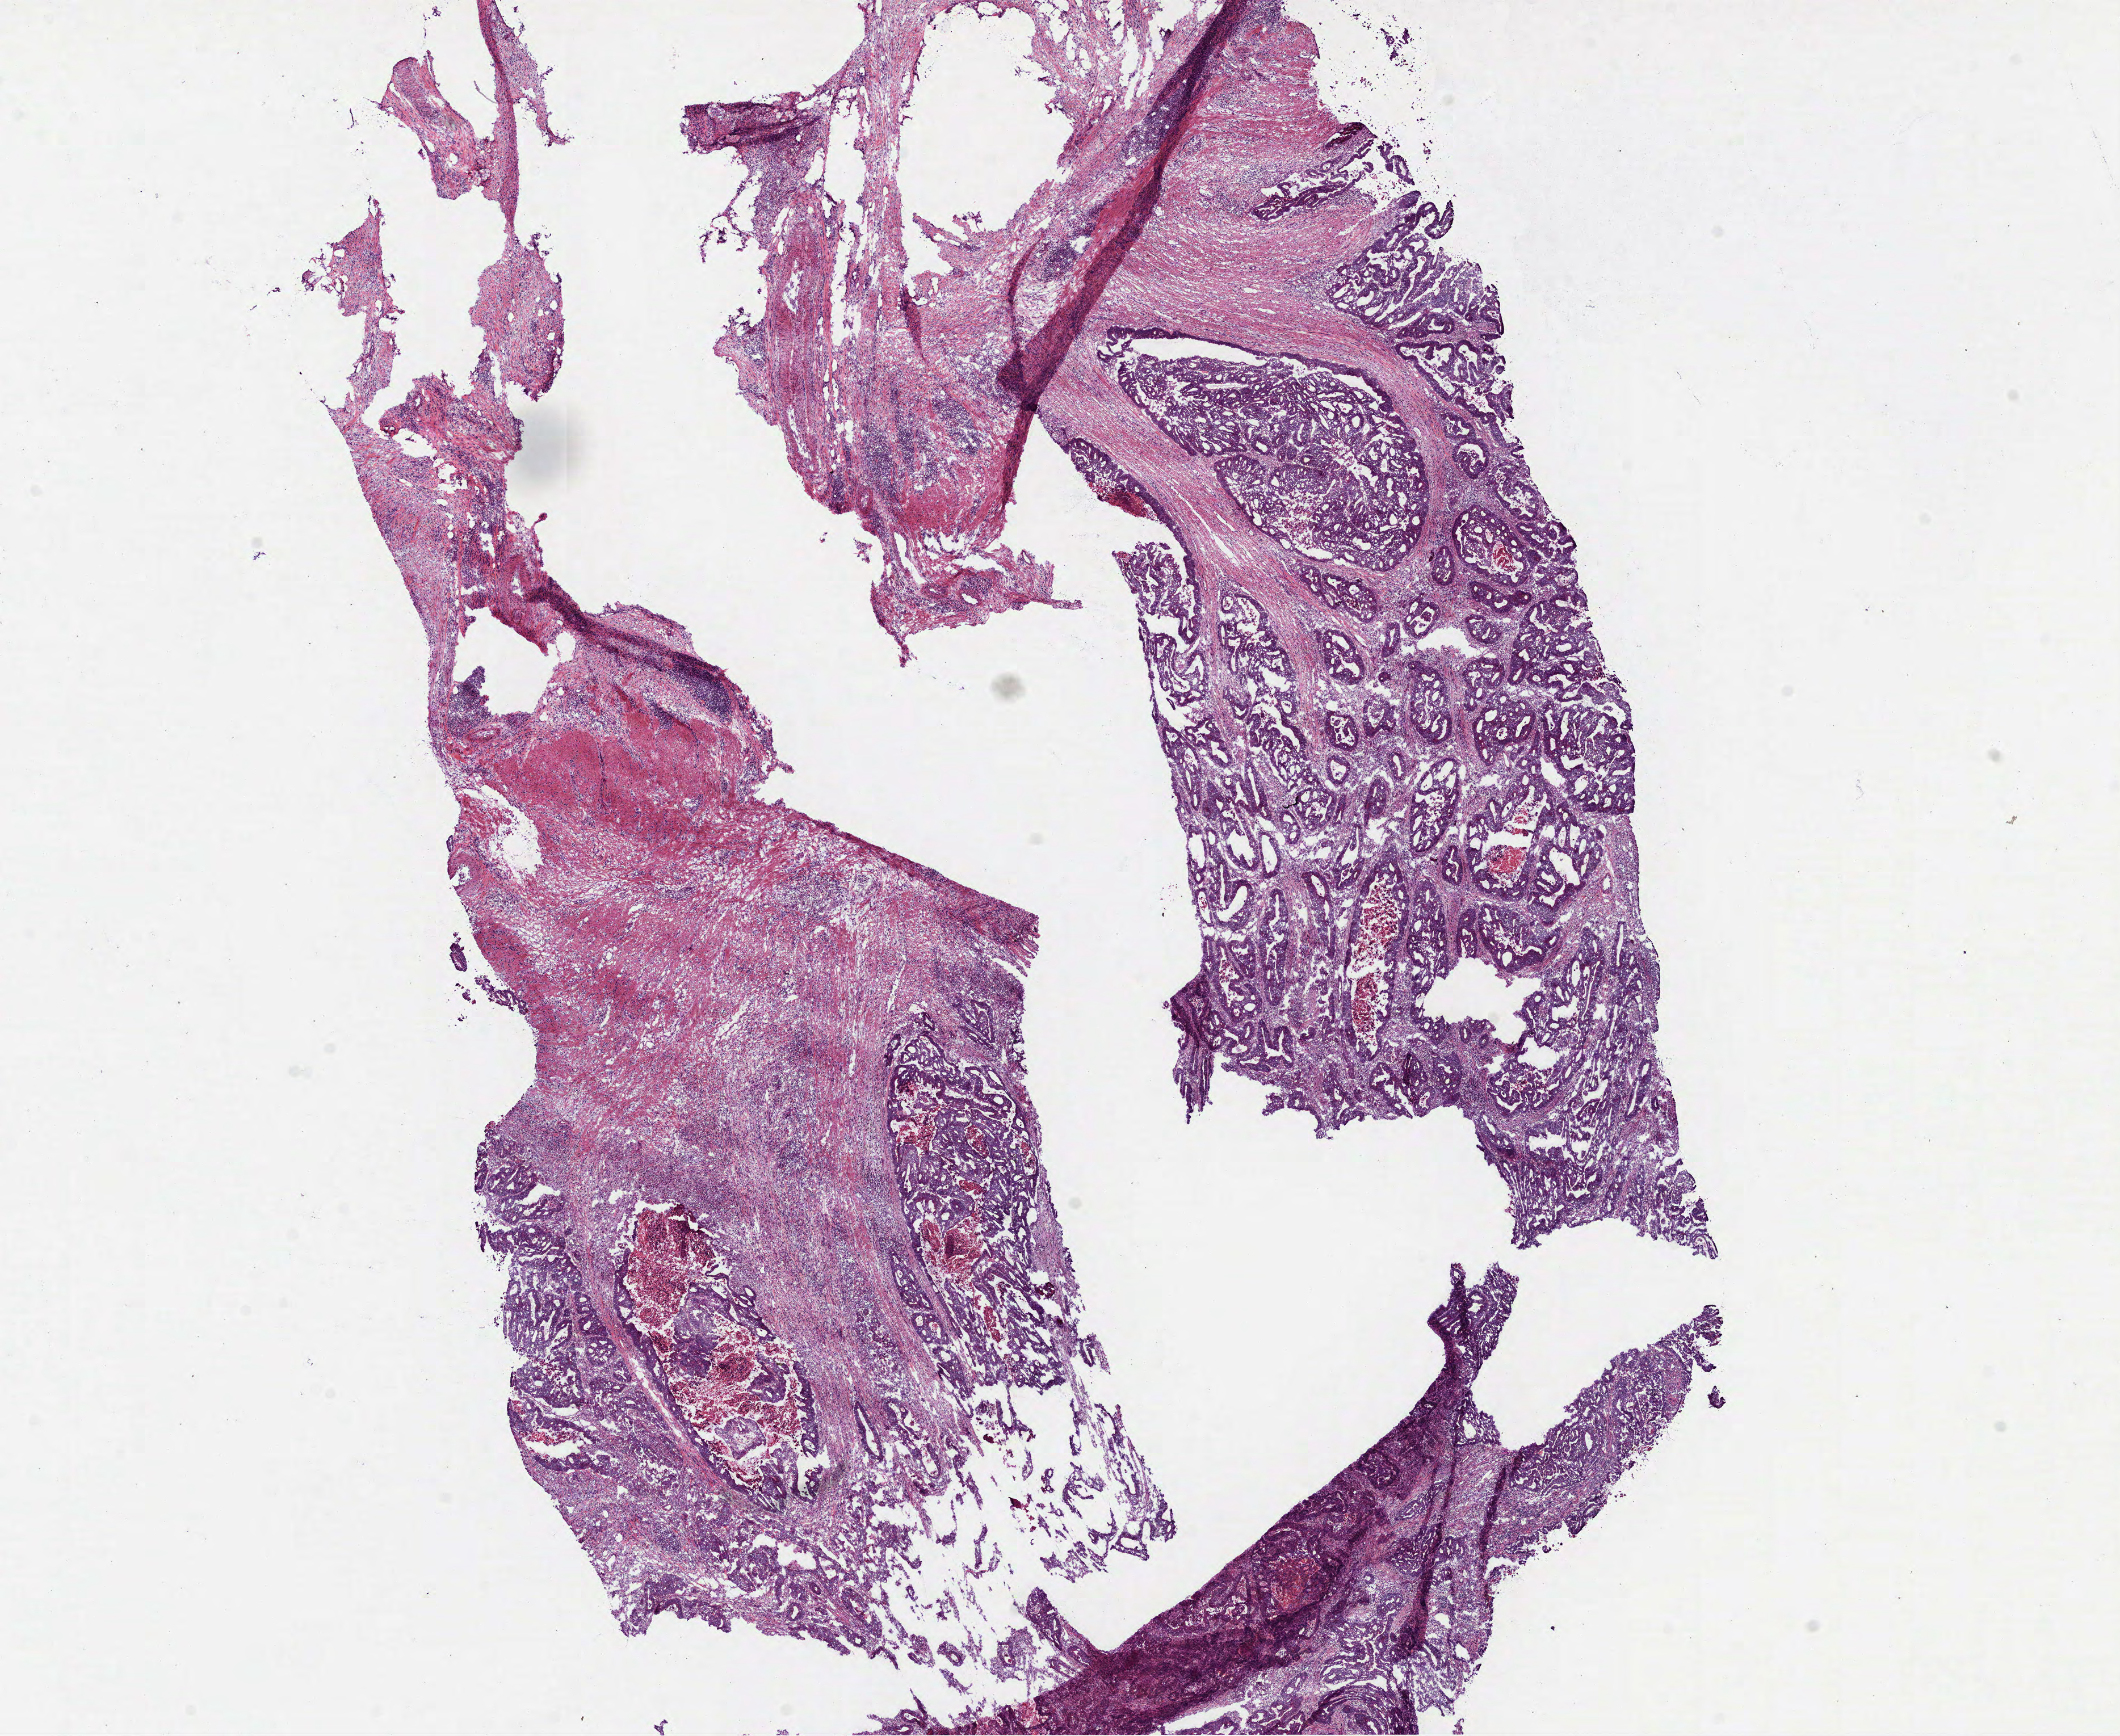
Digitized H&E-stained tissue section (whole slide) — whole scanned area (about 15.1 x 12.3 mm, from a 40x scan) shown as a low-resolution overview. Frozen section from the bottom of the tissue portion. Primary tumour sample from the rectum. Male patient; age at initial diagnosis 43 years. Pathologist review of this section (percent, as recorded): tumour cells 72%, tumour nuclei 70%, normal cells 0%, stromal cells 20%, necrosis 8%.
Pathologic diagnosis: Adenocarcinoma, NOS (rectosigmoid junction). AJCC pathologic stage: IIIB (7th edition). Lymph nodes positive (case pathology): 3 of 27 examined.